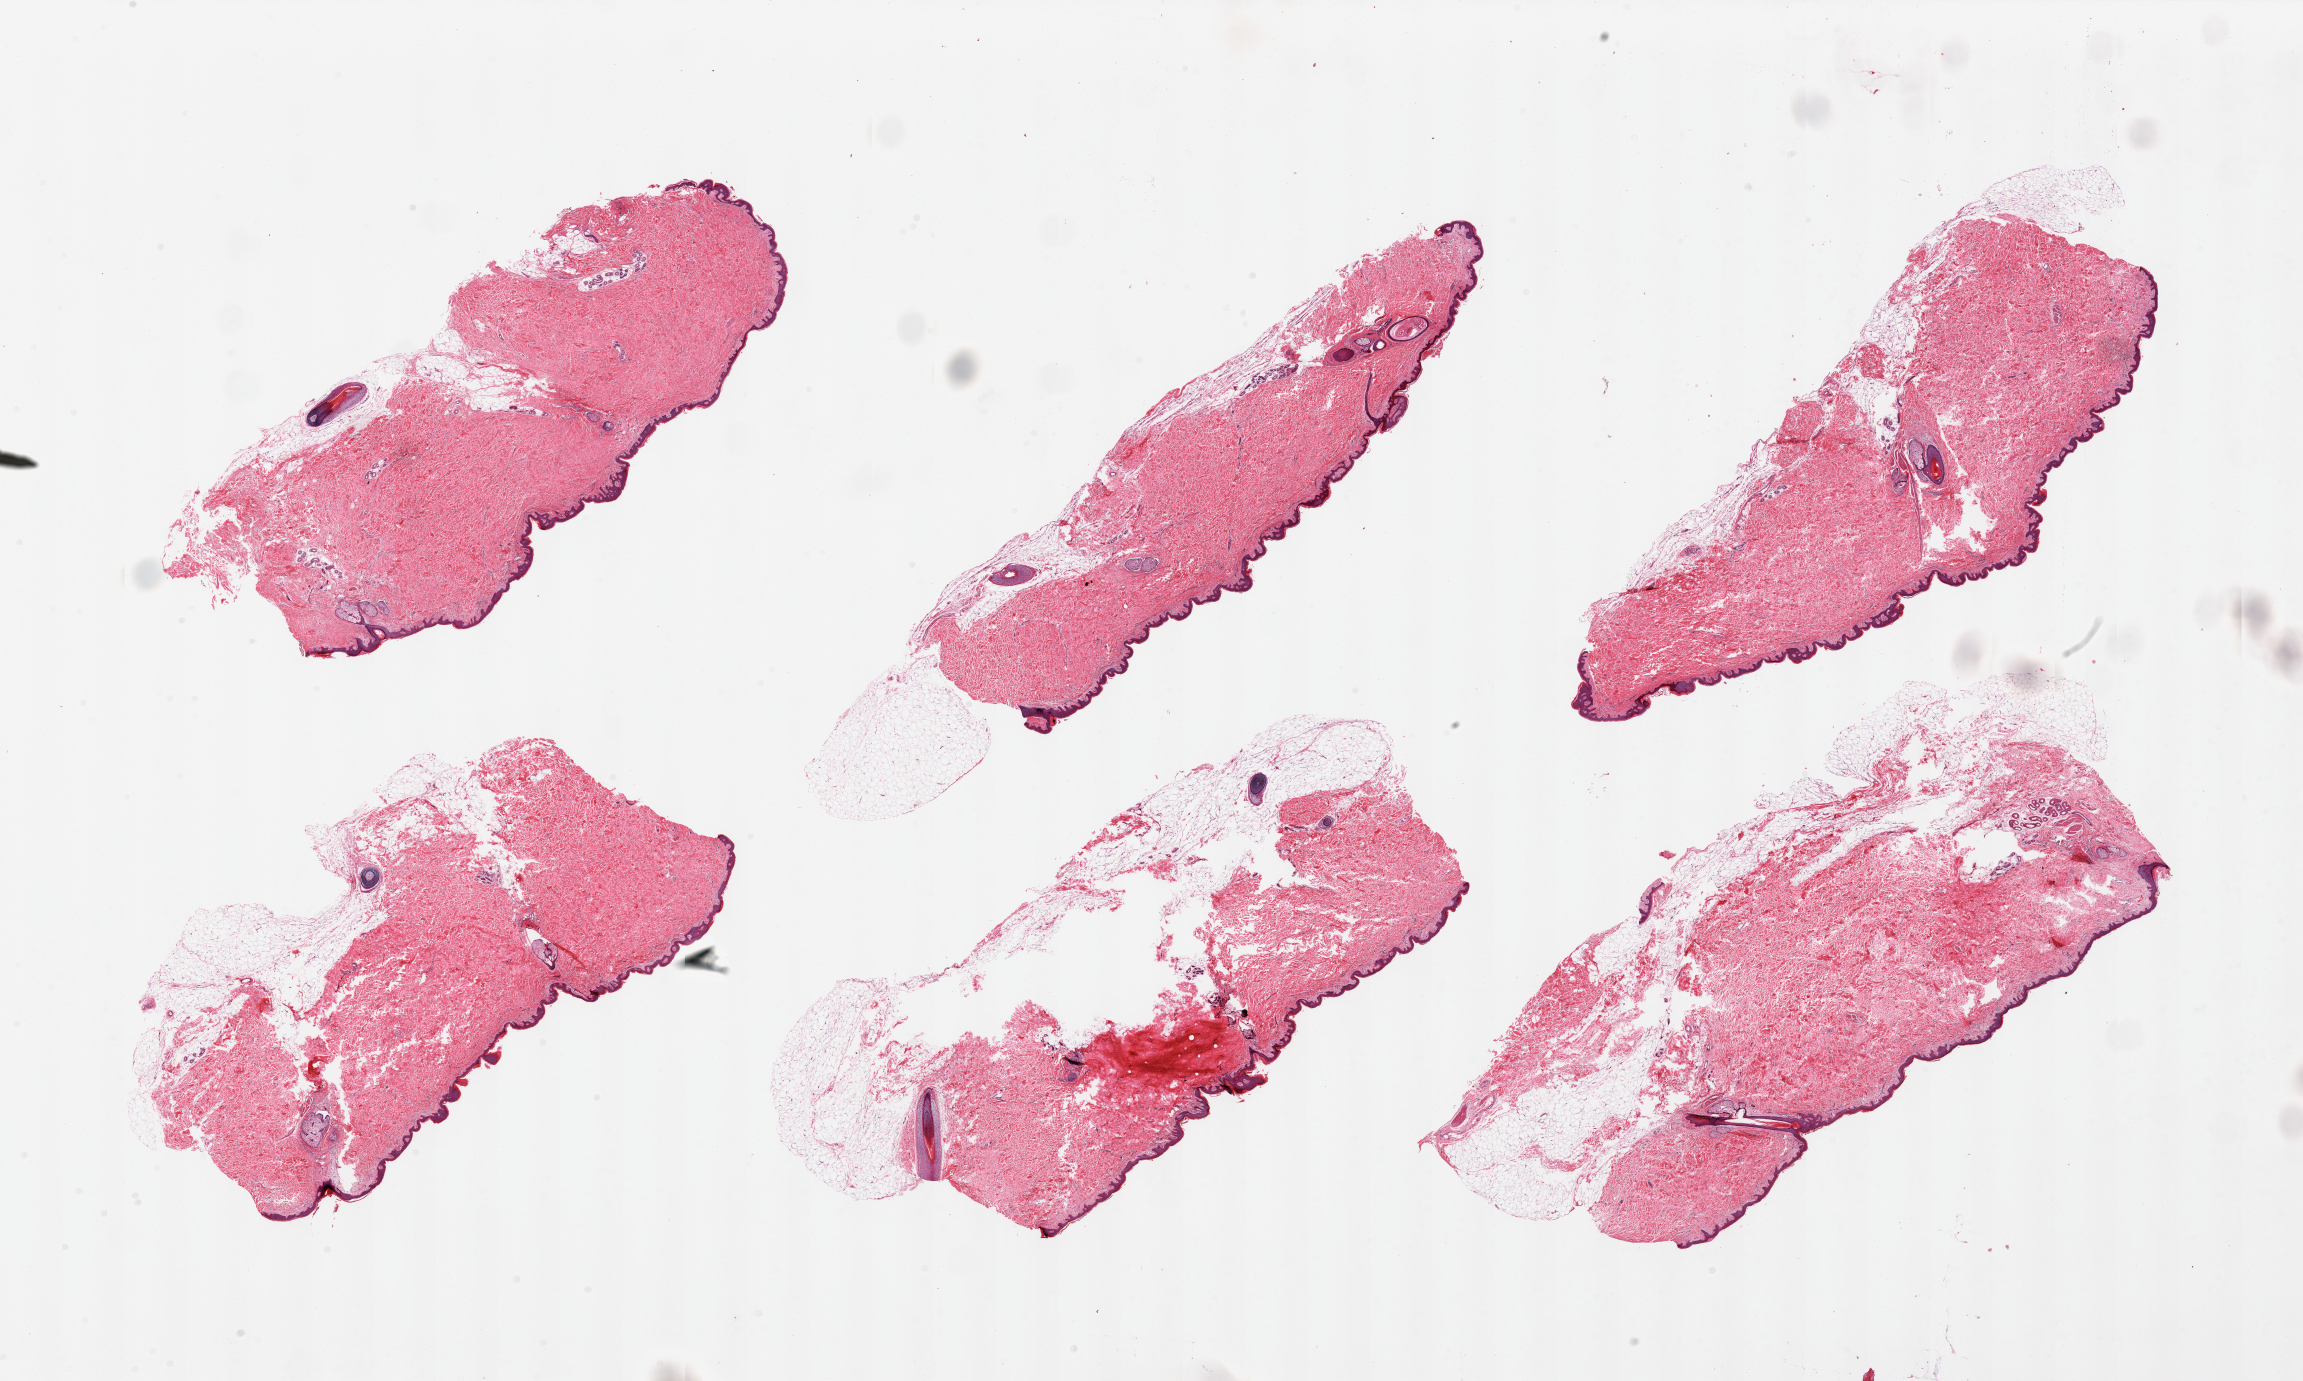
H&E whole-slide image — shown as a low-resolution overview of the whole scanned area (about 36.4 x 21.8 mm). PAXgene-fixed paraffin-embedded (PFPE) section. Target tissue: skin of suprapubic region. Tissue donor sample.
• pathologist's review note for this sample: 6 pieces, prominent adherent fat up to ~2mm on one section; squamous epithelium is ~70 microns